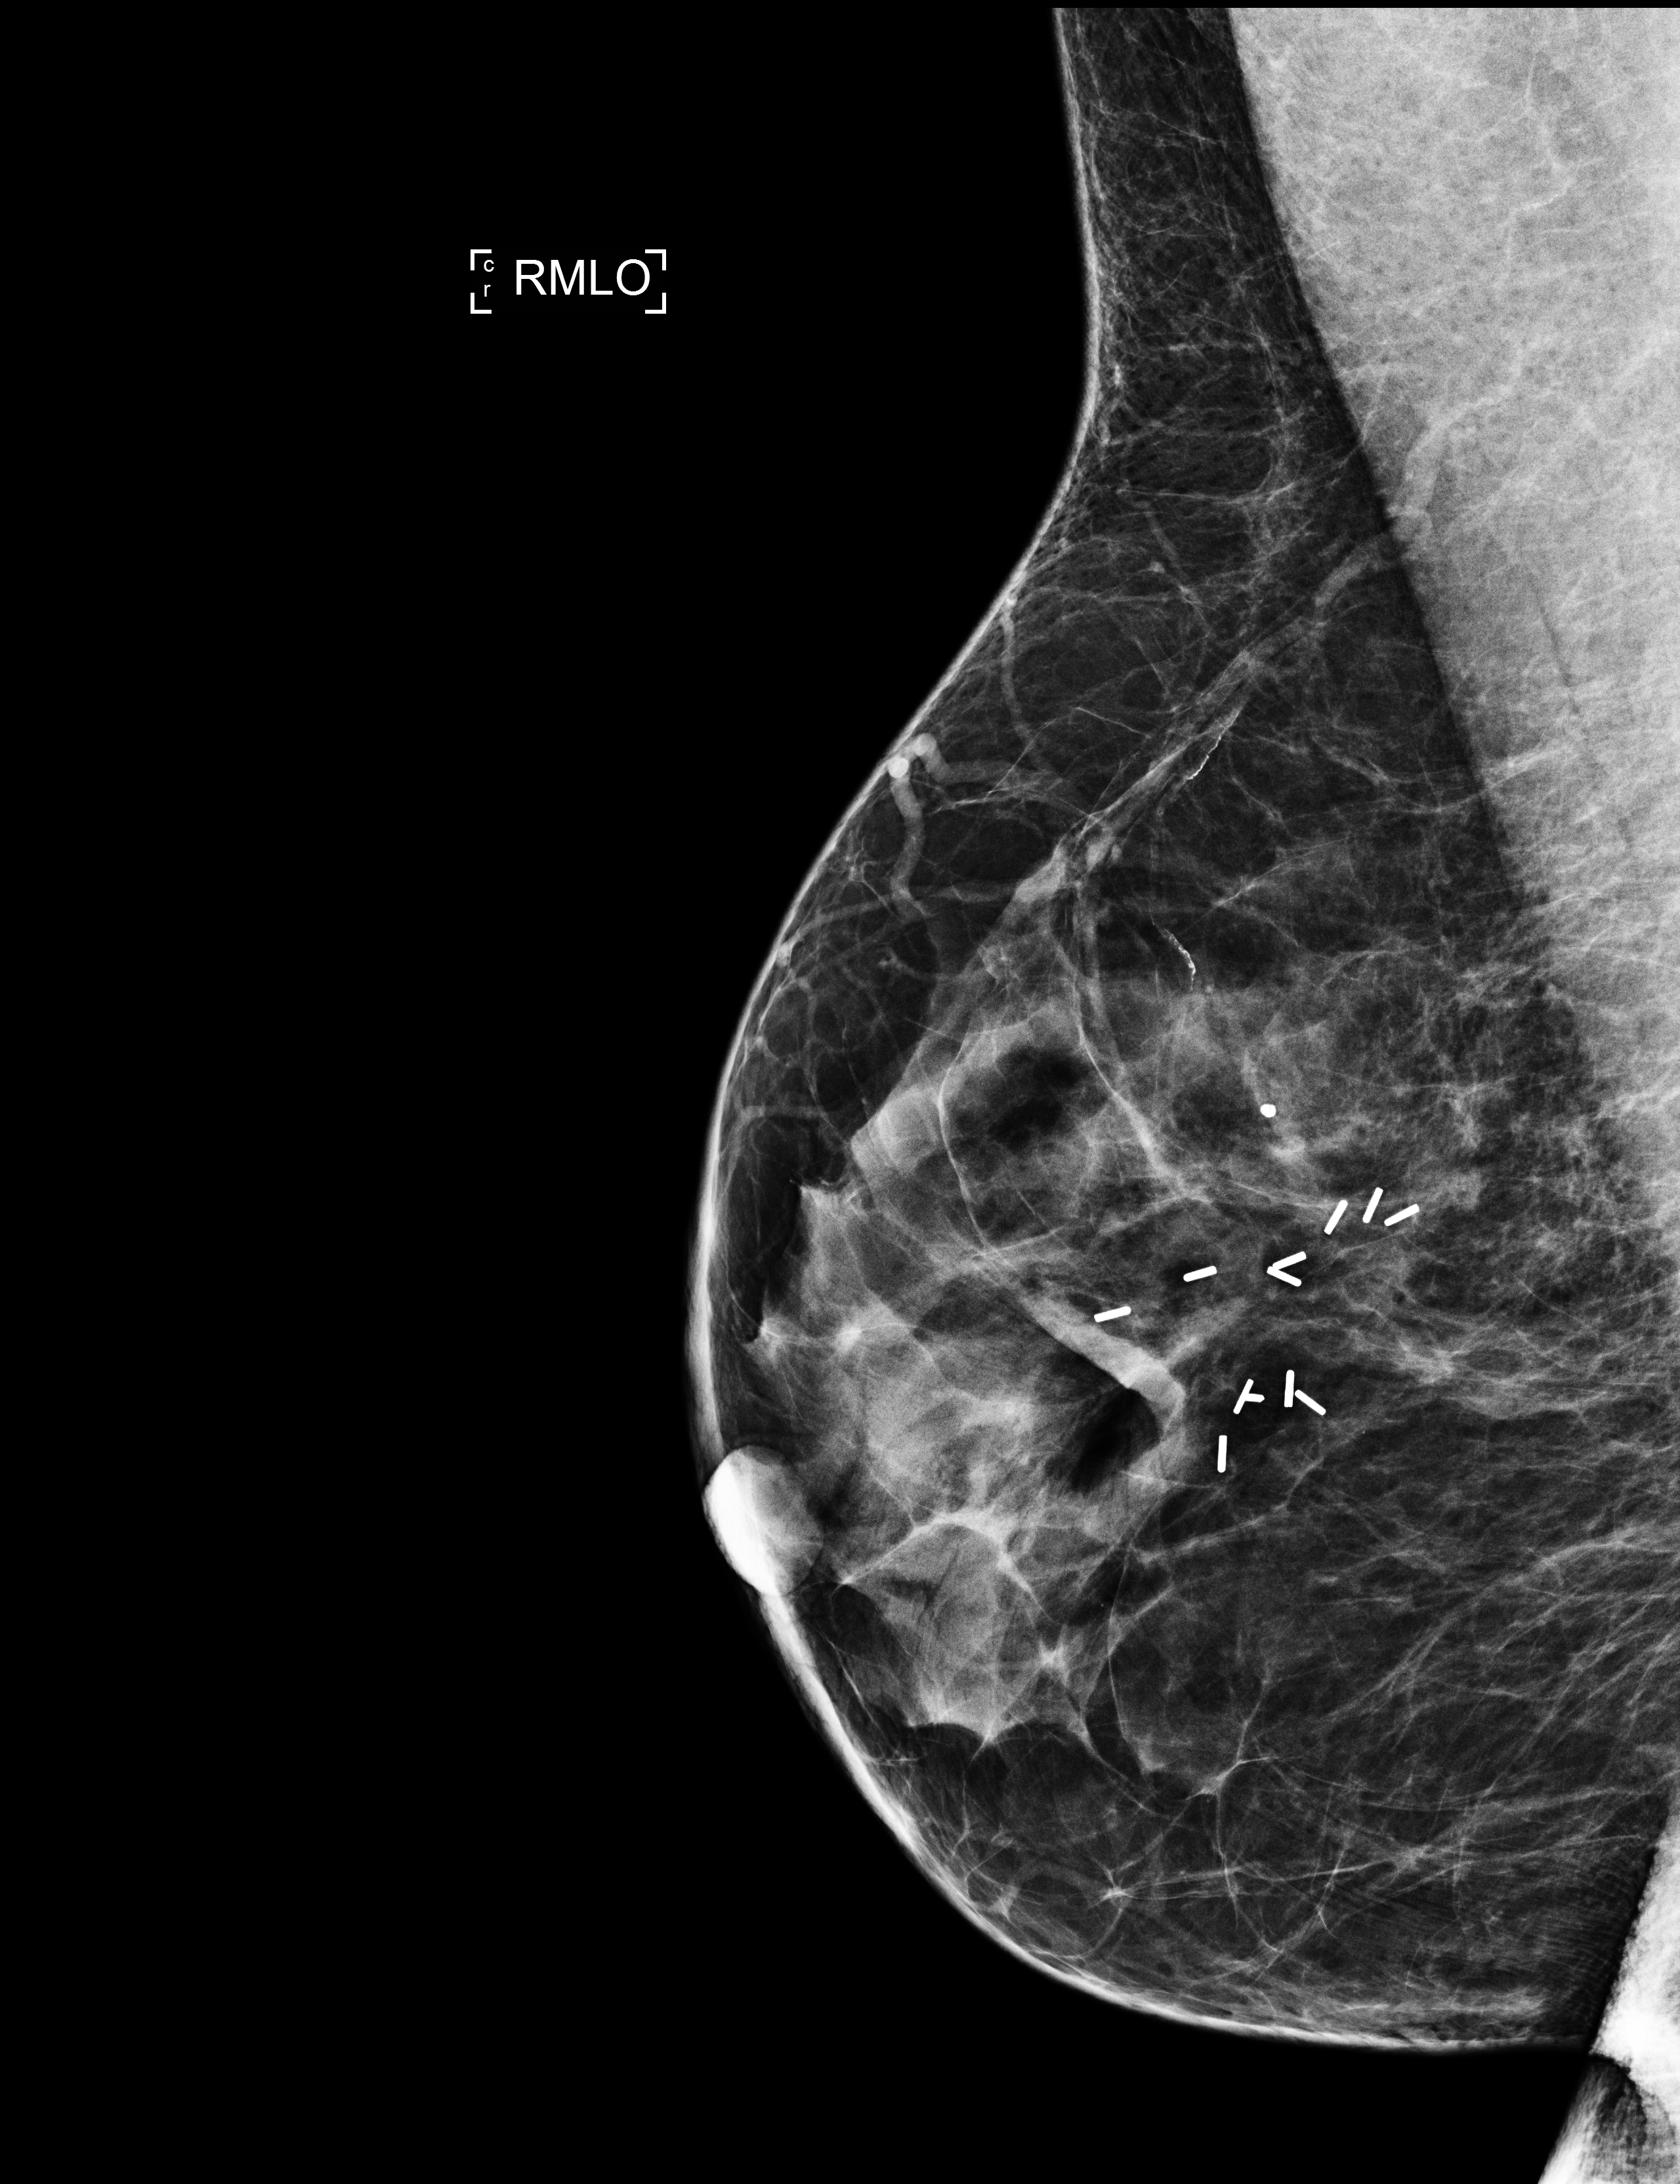
Screening examination; compressed breast thickness 46 mm; system: Selenia Dimensions. Female patient, age 49 years.
Image type: full-field digital mammogram. Breast: right. Projection: medio-lateral oblique projection.